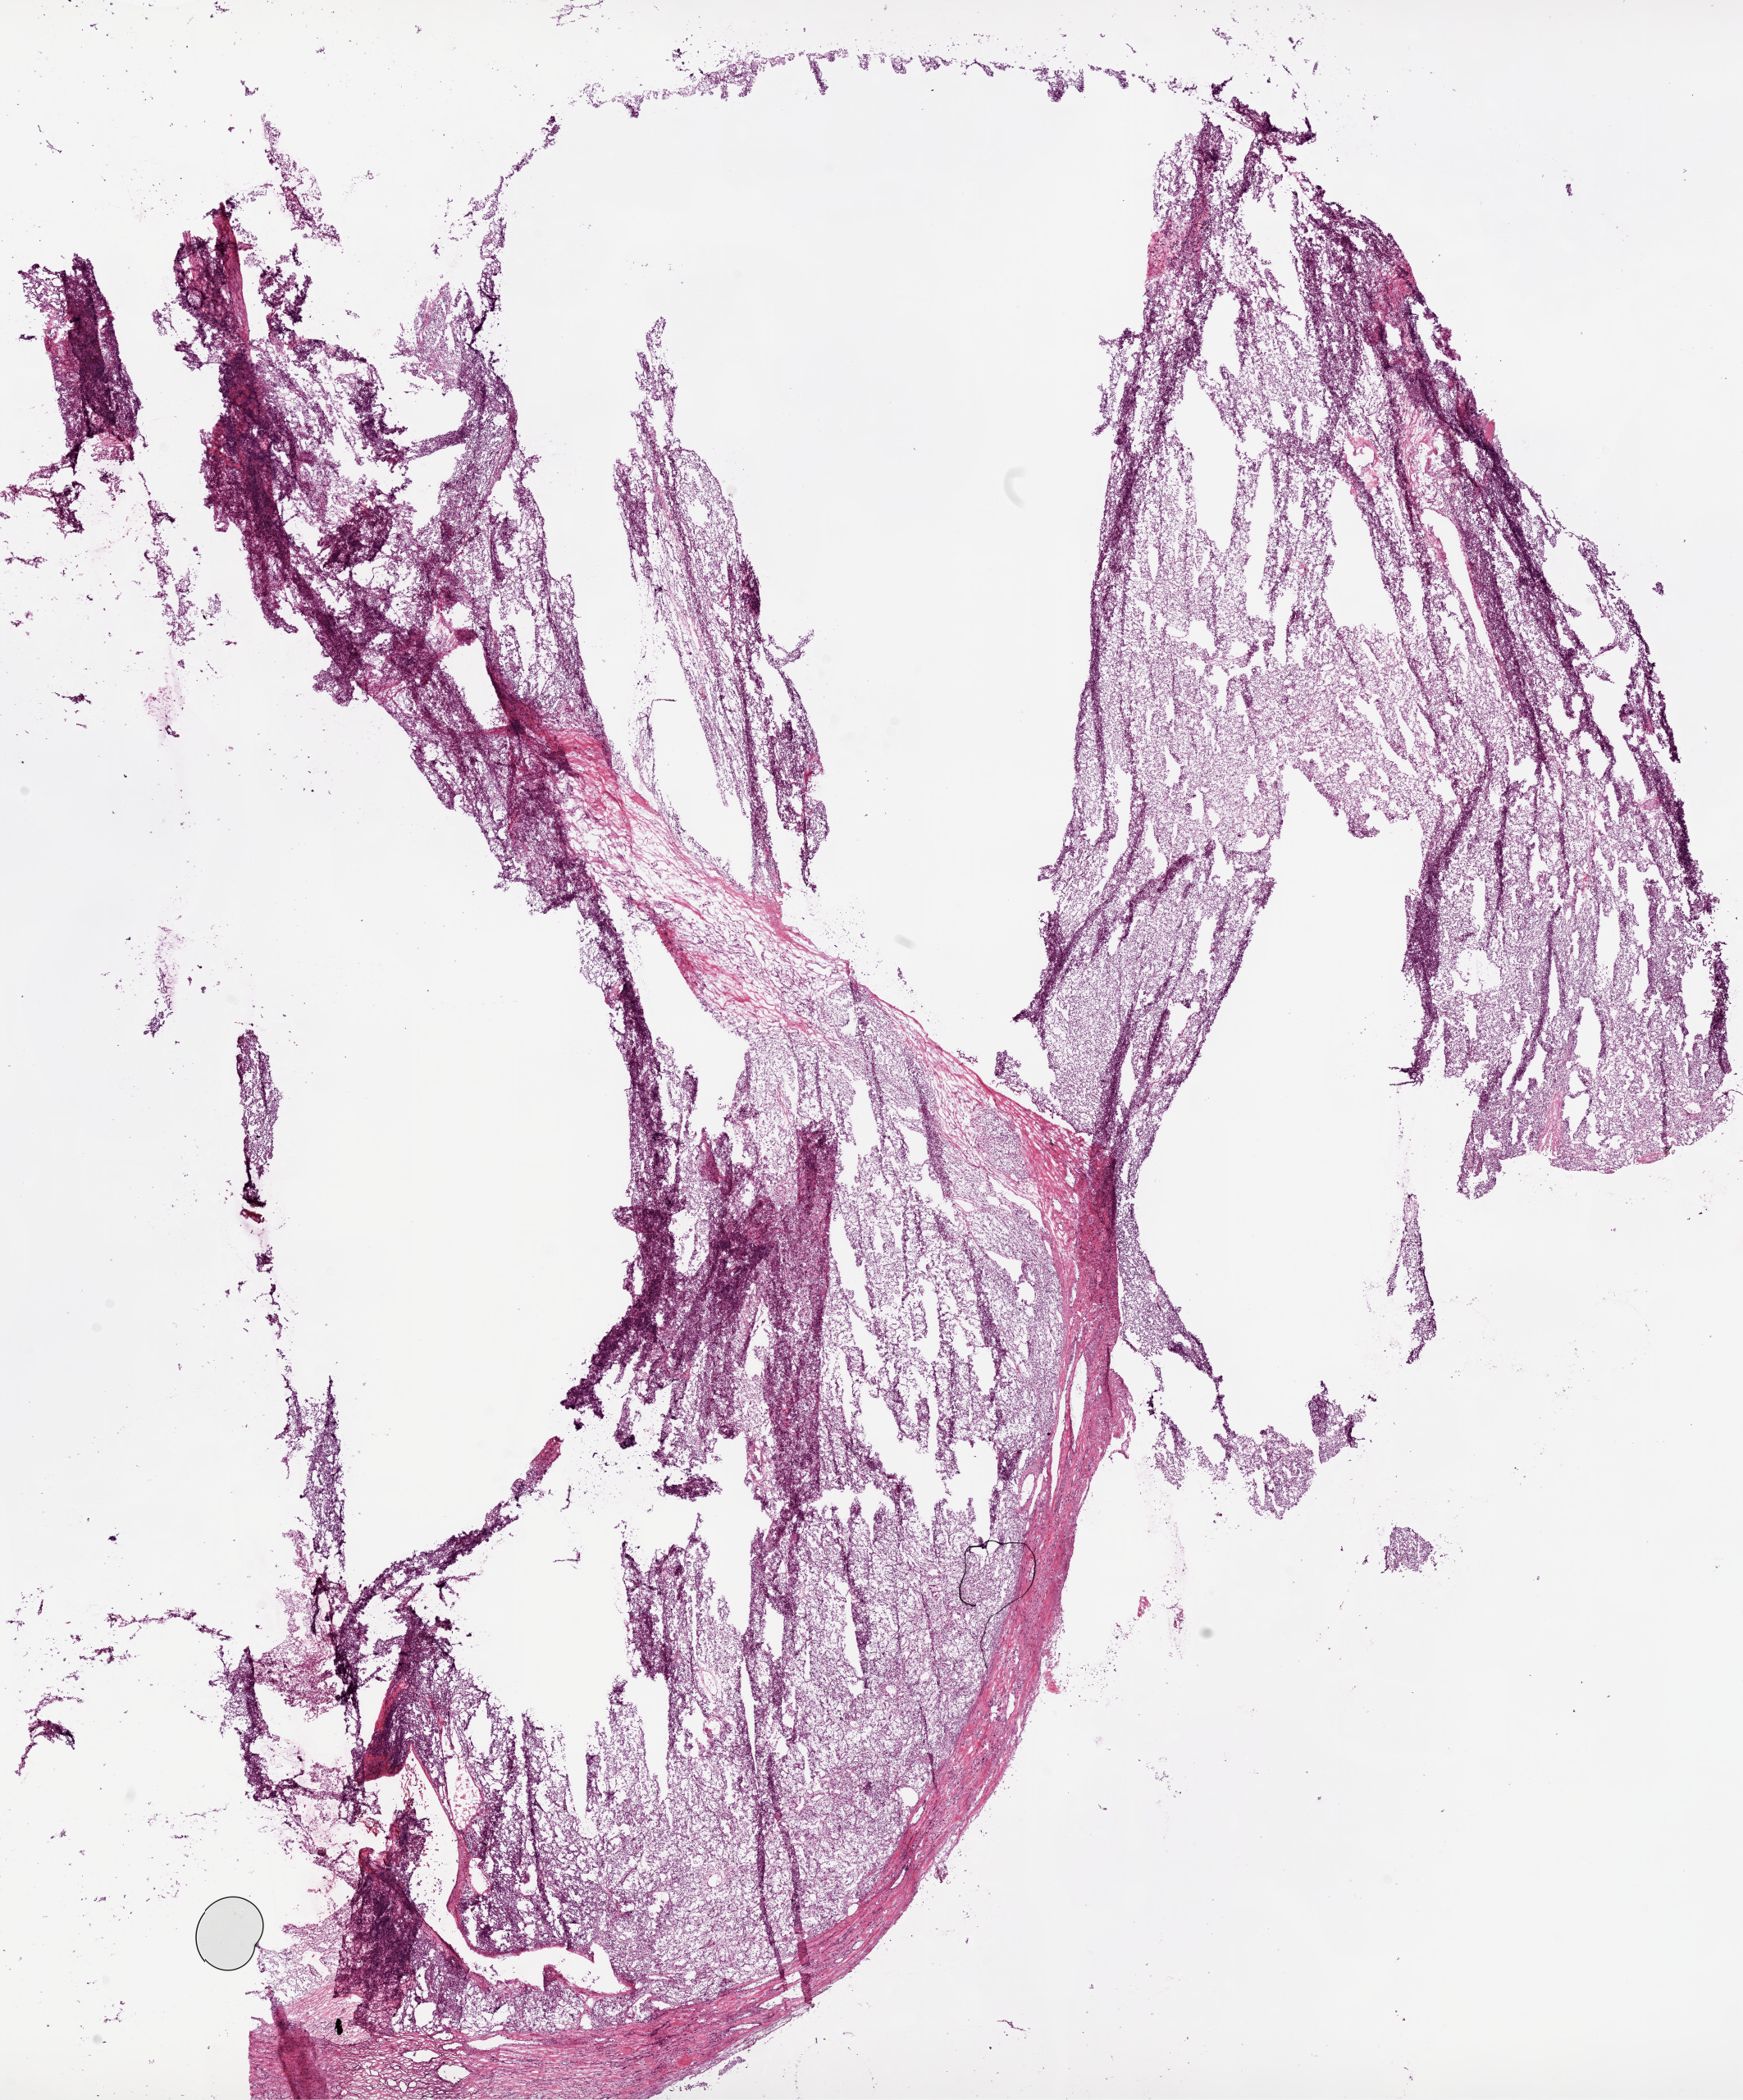
Digitized H&E-stained tissue section (whole slide), low-resolution overview of the scanned area, about 17.1 x 20.5 mm (acquisition: 20x scan). Frozen section from the bottom of the tissue portion. Kidney, primary tumour sample. Patient: female, age at initial diagnosis 61 years. Histologic grade: G2 (moderately differentiated). Composition of this section per pathologist review: tumour cells 85%, tumour nuclei 85%, normal cells 0%, stromal cells 15%, necrosis 0%.
Diagnosis: Clear cell adenocarcinoma, NOS. AJCC pathologic stage: I (6th edition).